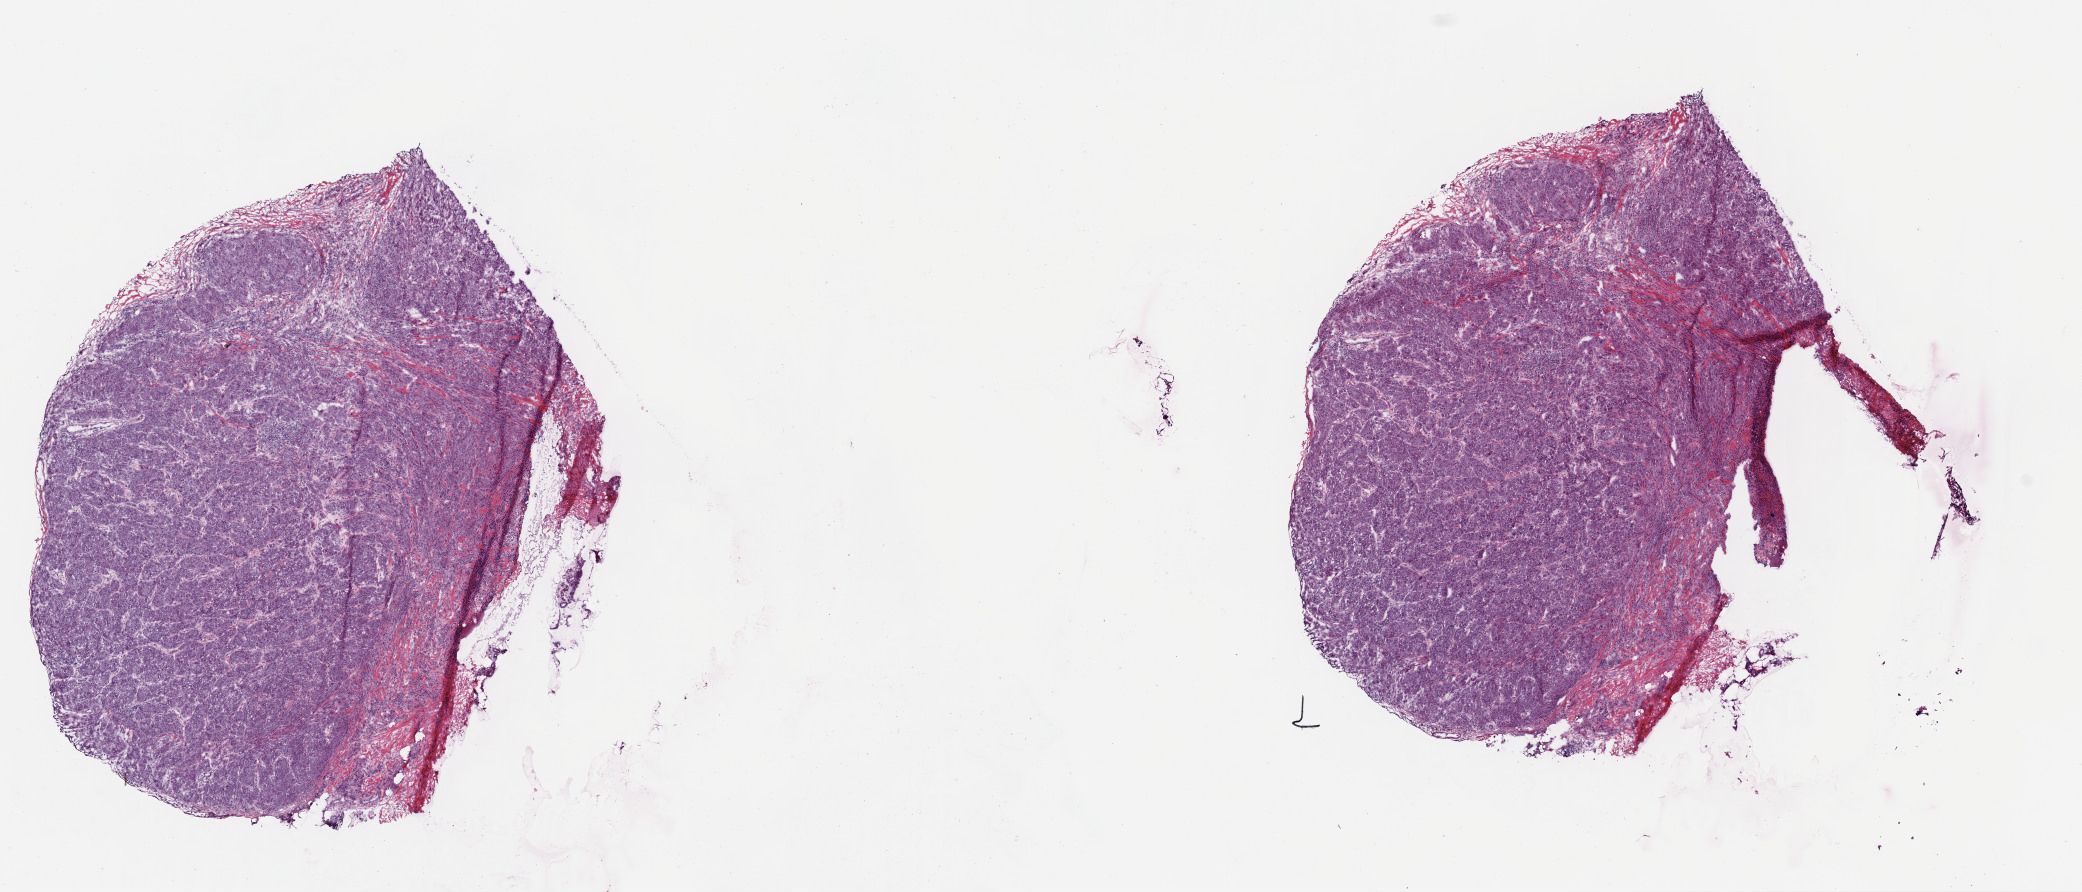
Digitized H&E tissue section (whole slide), low-resolution overview of the scanned area, about 16.4 x 7.0 mm, frozen section from the top of the tissue portion, metastatic tumour sample, sampled site: skin. Patient: female, age at initial diagnosis 75 years. Composition of this section per pathologist review: tumour cells 100%, tumour nuclei 95%, normal cells 0%, stromal cells 0%, necrosis 0%. Infiltration values recorded for this section: lymphocyte infiltration 0%, monocyte infiltration 0%, neutrophil infiltration 0%.
- this section: metastatic tumour tissue
- patient diagnosis: Malignant melanoma, NOS